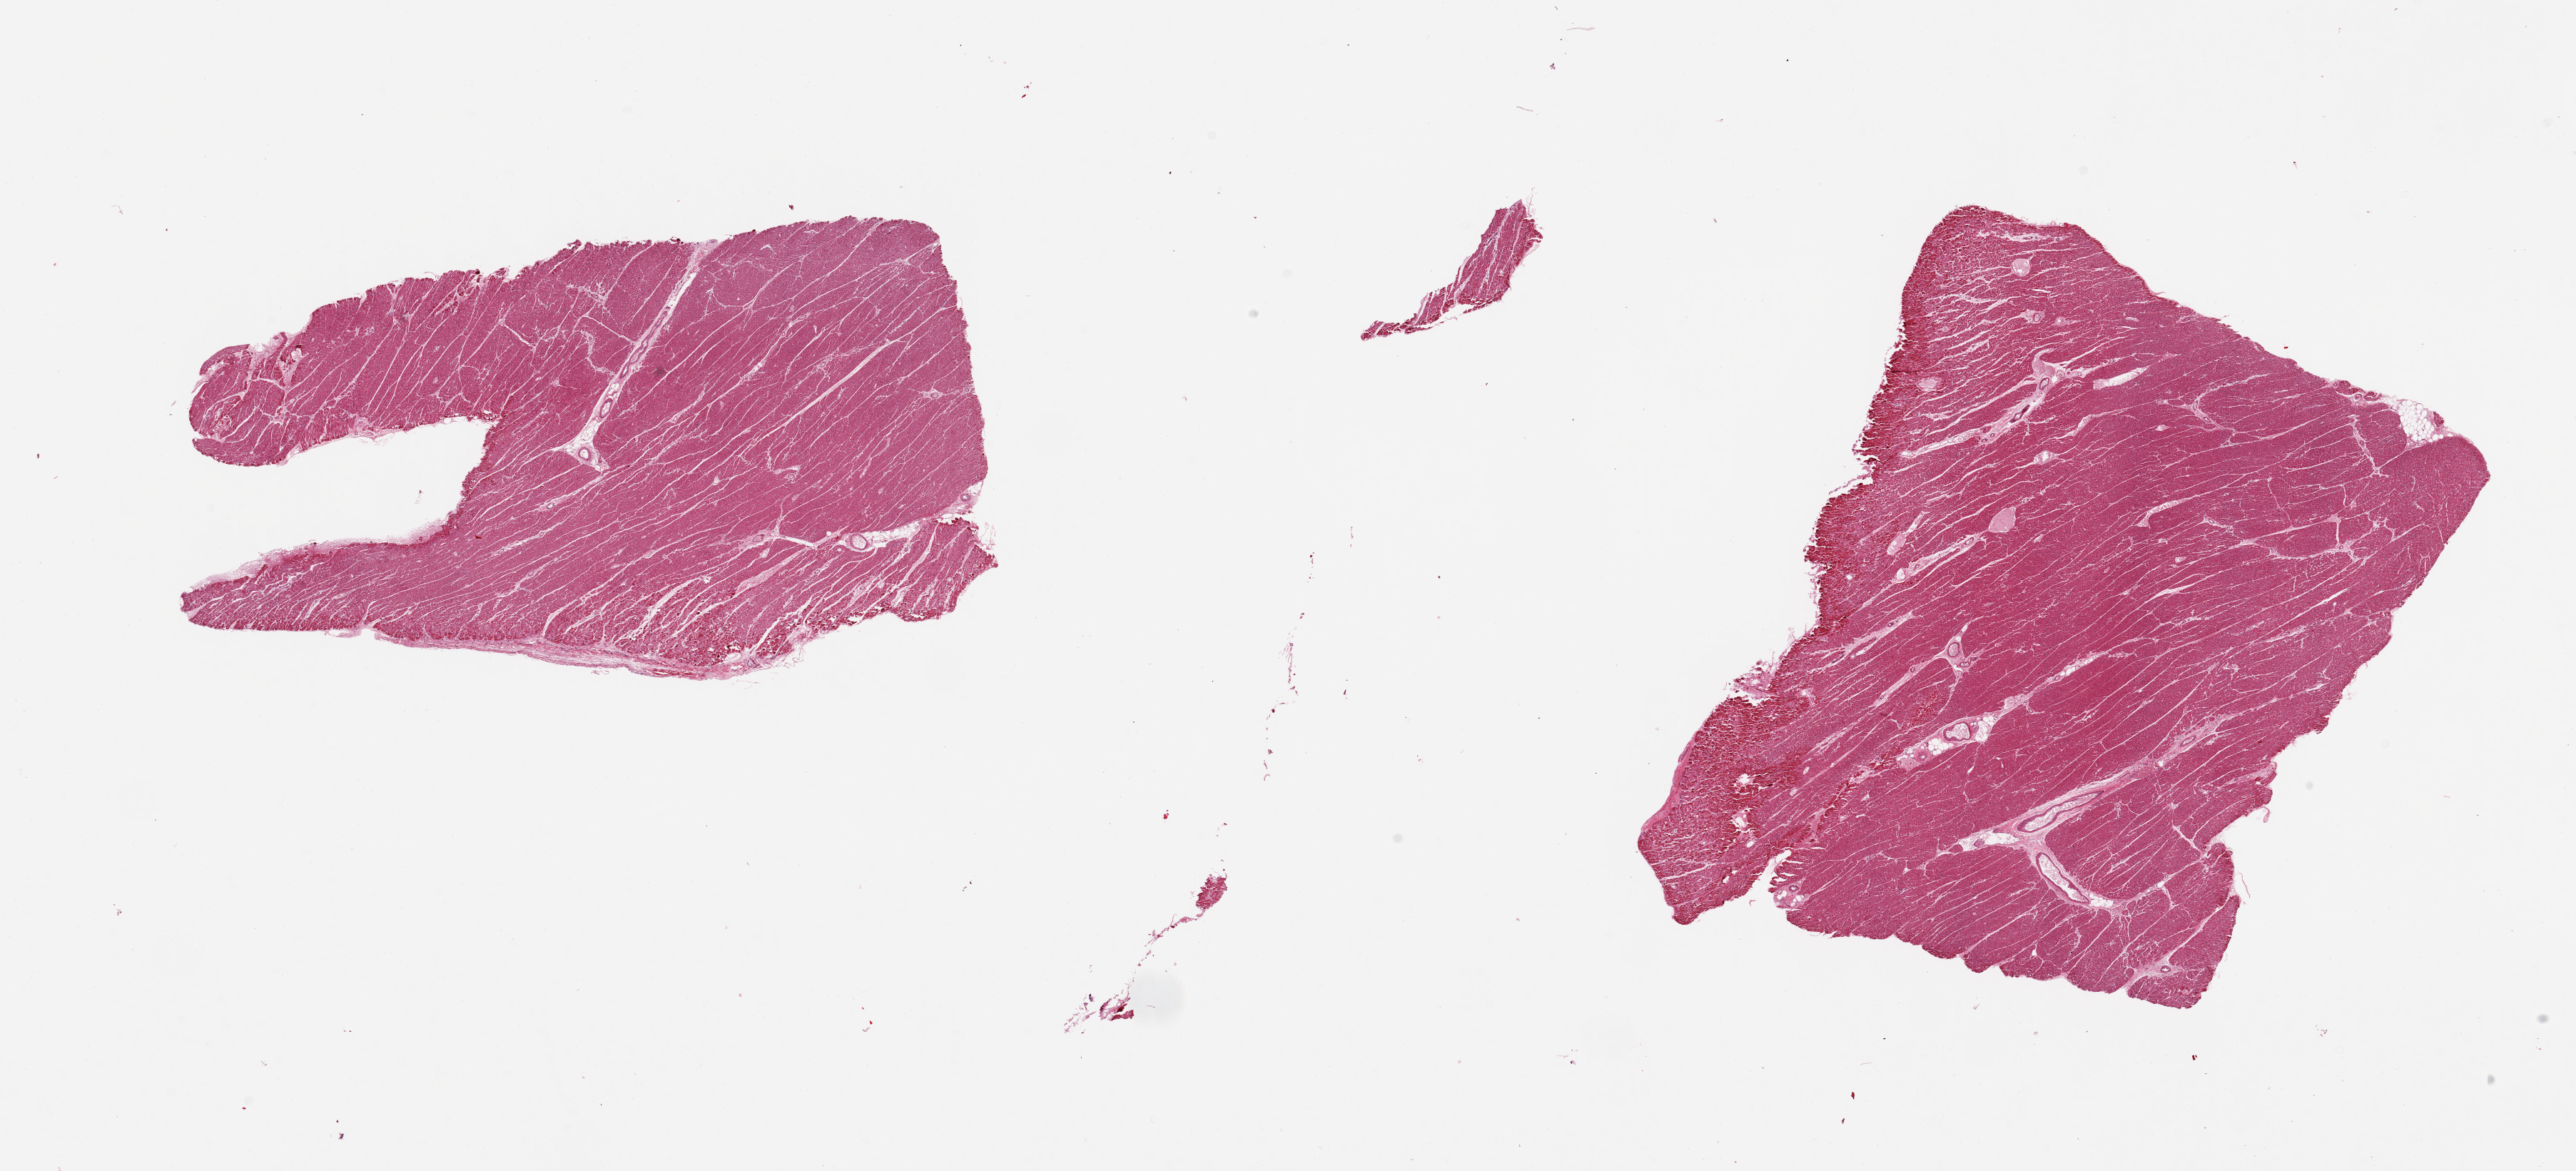
Whole-slide image, H&E stain, brightfield, low-resolution overview of the scanned area, about 28.5 x 13.0 mm; PAXgene-fixed paraffin-embedded (PFPE) section; sampled site (target tissue): heart; donor tissue sample. Donor sex: female.
Reviewer comment on this tissue sample: 2 pieces; appears to represent heart specimen, not atrial appendage.